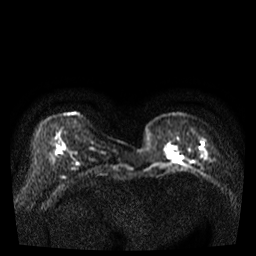
Breast MRI, one axial slice; slice 8 of 35 in the series (ordered by position); diffusion-weighted series; image 2 of 4 stored at this slice position (different b-values; order by instance number); 3 T; 256 × 256 image matrix, field of view 320 × 320 mm. Female patient.
Annotated regions visible in this slice (expert manual segmentation):
- tumour on diffusion-weighted imaging: bounding box [x1, y1, x2, y2] px = [169, 147, 181, 162]